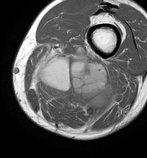
MRI of an extremity soft-tissue mass, one axial slice. Slice 28 of 86 in the series (ordered by position). MR volume resampled by the dataset authors to the PET/CT grid (not the native acquisition matrix). 3.27 mm slice thickness. 147 × 158 image matrix. Male patient. Case-level facts recorded for this patient, not image findings: histological type: undifferentiated pleomorphic liposarcoma; grade: high; site of the primary tumour: left thigh.
Annotated regions visible in this slice (expert contour drawn on MRI and transferred to this co-registered scan by the dataset authors):
- gross tumour volume including surrounding oedema: bounding box (x1, y1, x2, y2) in pixels: (30, 44, 118, 125)
- gross tumour volume (mass): (39, 58, 108, 109)